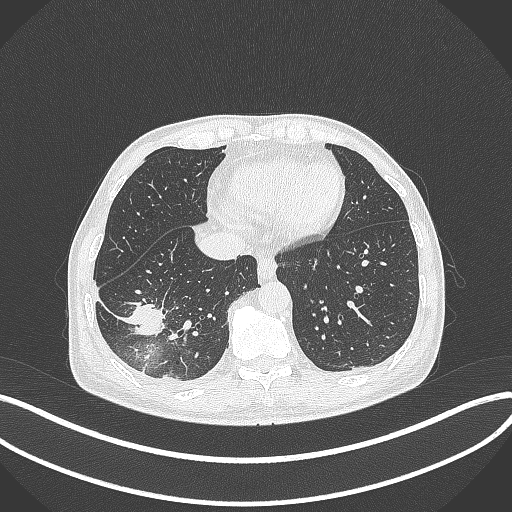
Chest CT, one axial slice. Slice 103 of 388 in the series (ordered by position). 120 kVp. Lung window (W 1500 / L -600 HU). 512 × 512 image matrix, field of view 400 × 400 mm. Patient: male, 64 years. Case-level facts recorded for this patient, not image findings: clinical TNM (as recorded): T3 N0 M0.
Structures marked on this image (bounding box drawn by a radiologist):
- lung tumour (recorded histology: adenocarcinoma): bounding box [x1, y1, x2, y2] px = [124, 296, 169, 343]